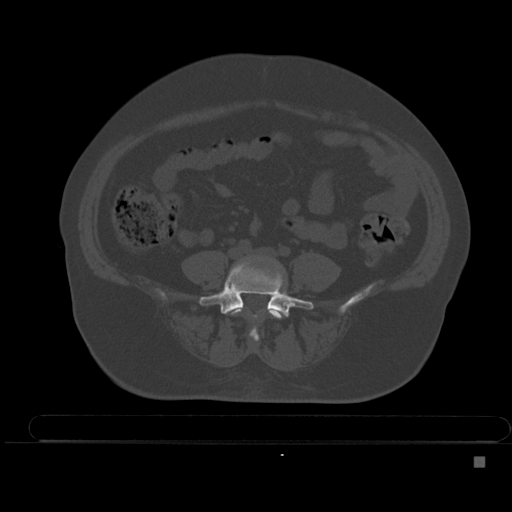
CT including the spine, one axial slice. Position 116 of 495 along the scan axis. Bone window (W 1800 / L 400 HU). 1.5 mm slice thickness. 512 × 512 image matrix, field of view 404 × 404 mm. Patient: female, 33 years. Case-level facts recorded for this patient, not image findings: primary cancer: breast.
Annotated regions visible in this slice (semi-automatically segmented with operator editing):
- L4 vertebra: bounding box <229,308,285,342> (left, top, right, bottom; pixels)
- L5 vertebra: <199,261,314,317>